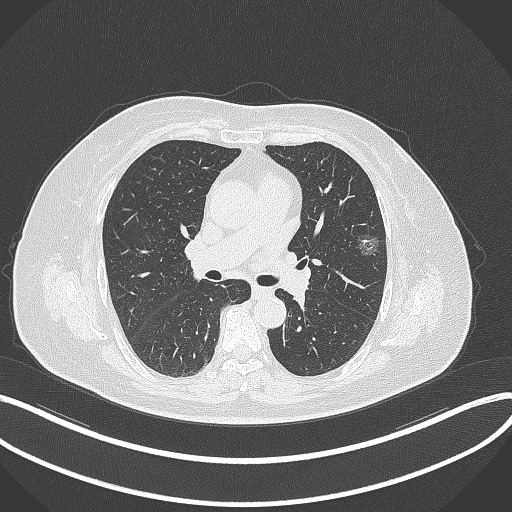
Chest CT, one axial slice; slice 209 of 315 in the series (ordered by position); reconstruction kernel B70f; 120 kVp; lung window (W 1500 / L -600 HU); 1 mm slice thickness; 512 × 512 image matrix, field of view 400 × 400 mm. Patient: female, 76 years. From the clinical record (not read from this slice): clinical TNM (as recorded): T1b N0 M0; histopathological grade: G1-2.
Structures marked on this image (rectangle marked by the reading radiologist):
- lung tumour (recorded histology: adenocarcinoma): bounding box [x1, y1, x2, y2] px = [358, 231, 381, 259]